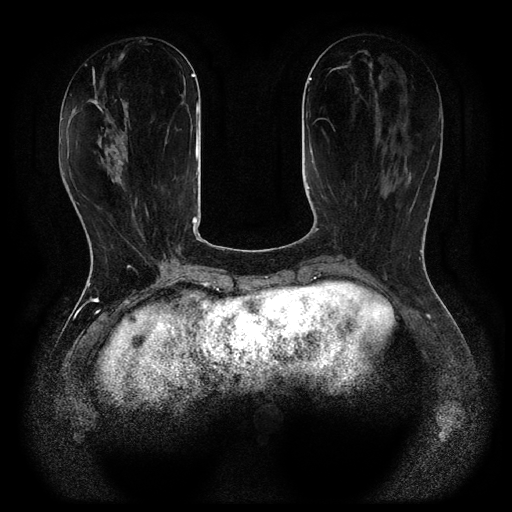
Breast MRI (dynamic contrast-enhanced, multi-phase), one axial slice; position 36 of 116 along the scan axis; dynamic contrast-enhanced series, time point 2 of 5 at this slice position (early post-contrast); 1.5 T; TE 2.6 ms, TR 5.4 ms; 2 mm slice thickness; 512 × 512 image matrix, field of view 340 × 340 mm. Patient: female, 48 years.
Annotated regions visible in this slice (semi-automatically segmented with operator editing):
- breast lesion (labelled benign in the annotation): box from (x=96, y=108) to (x=132, y=188) px